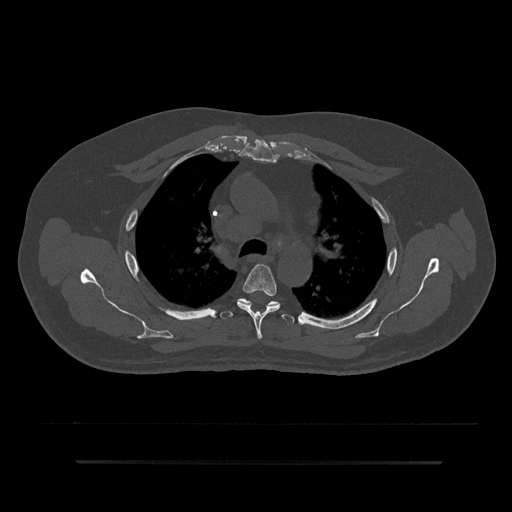
CT including the spine, one axial slice. Slice 607 of 797 in the series (ordered by position). Reconstruction kernel Br40s/3. Bone window (W 1800 / L 400 HU). 0.5 mm slice thickness. 512 × 512 image matrix, field of view 464 × 464 mm. Male patient, age 59 years. From the clinical record (not read from this slice): primary cancer: bile ducts; vertebrae with lytic lesions (as recorded): T10.
Annotated regions visible in this slice (semi-automatically segmented with operator editing):
- T4 vertebra: box from (x=237, y=264) to (x=280, y=339) px
- T5 vertebra: (x=220, y=298)–(x=294, y=323)